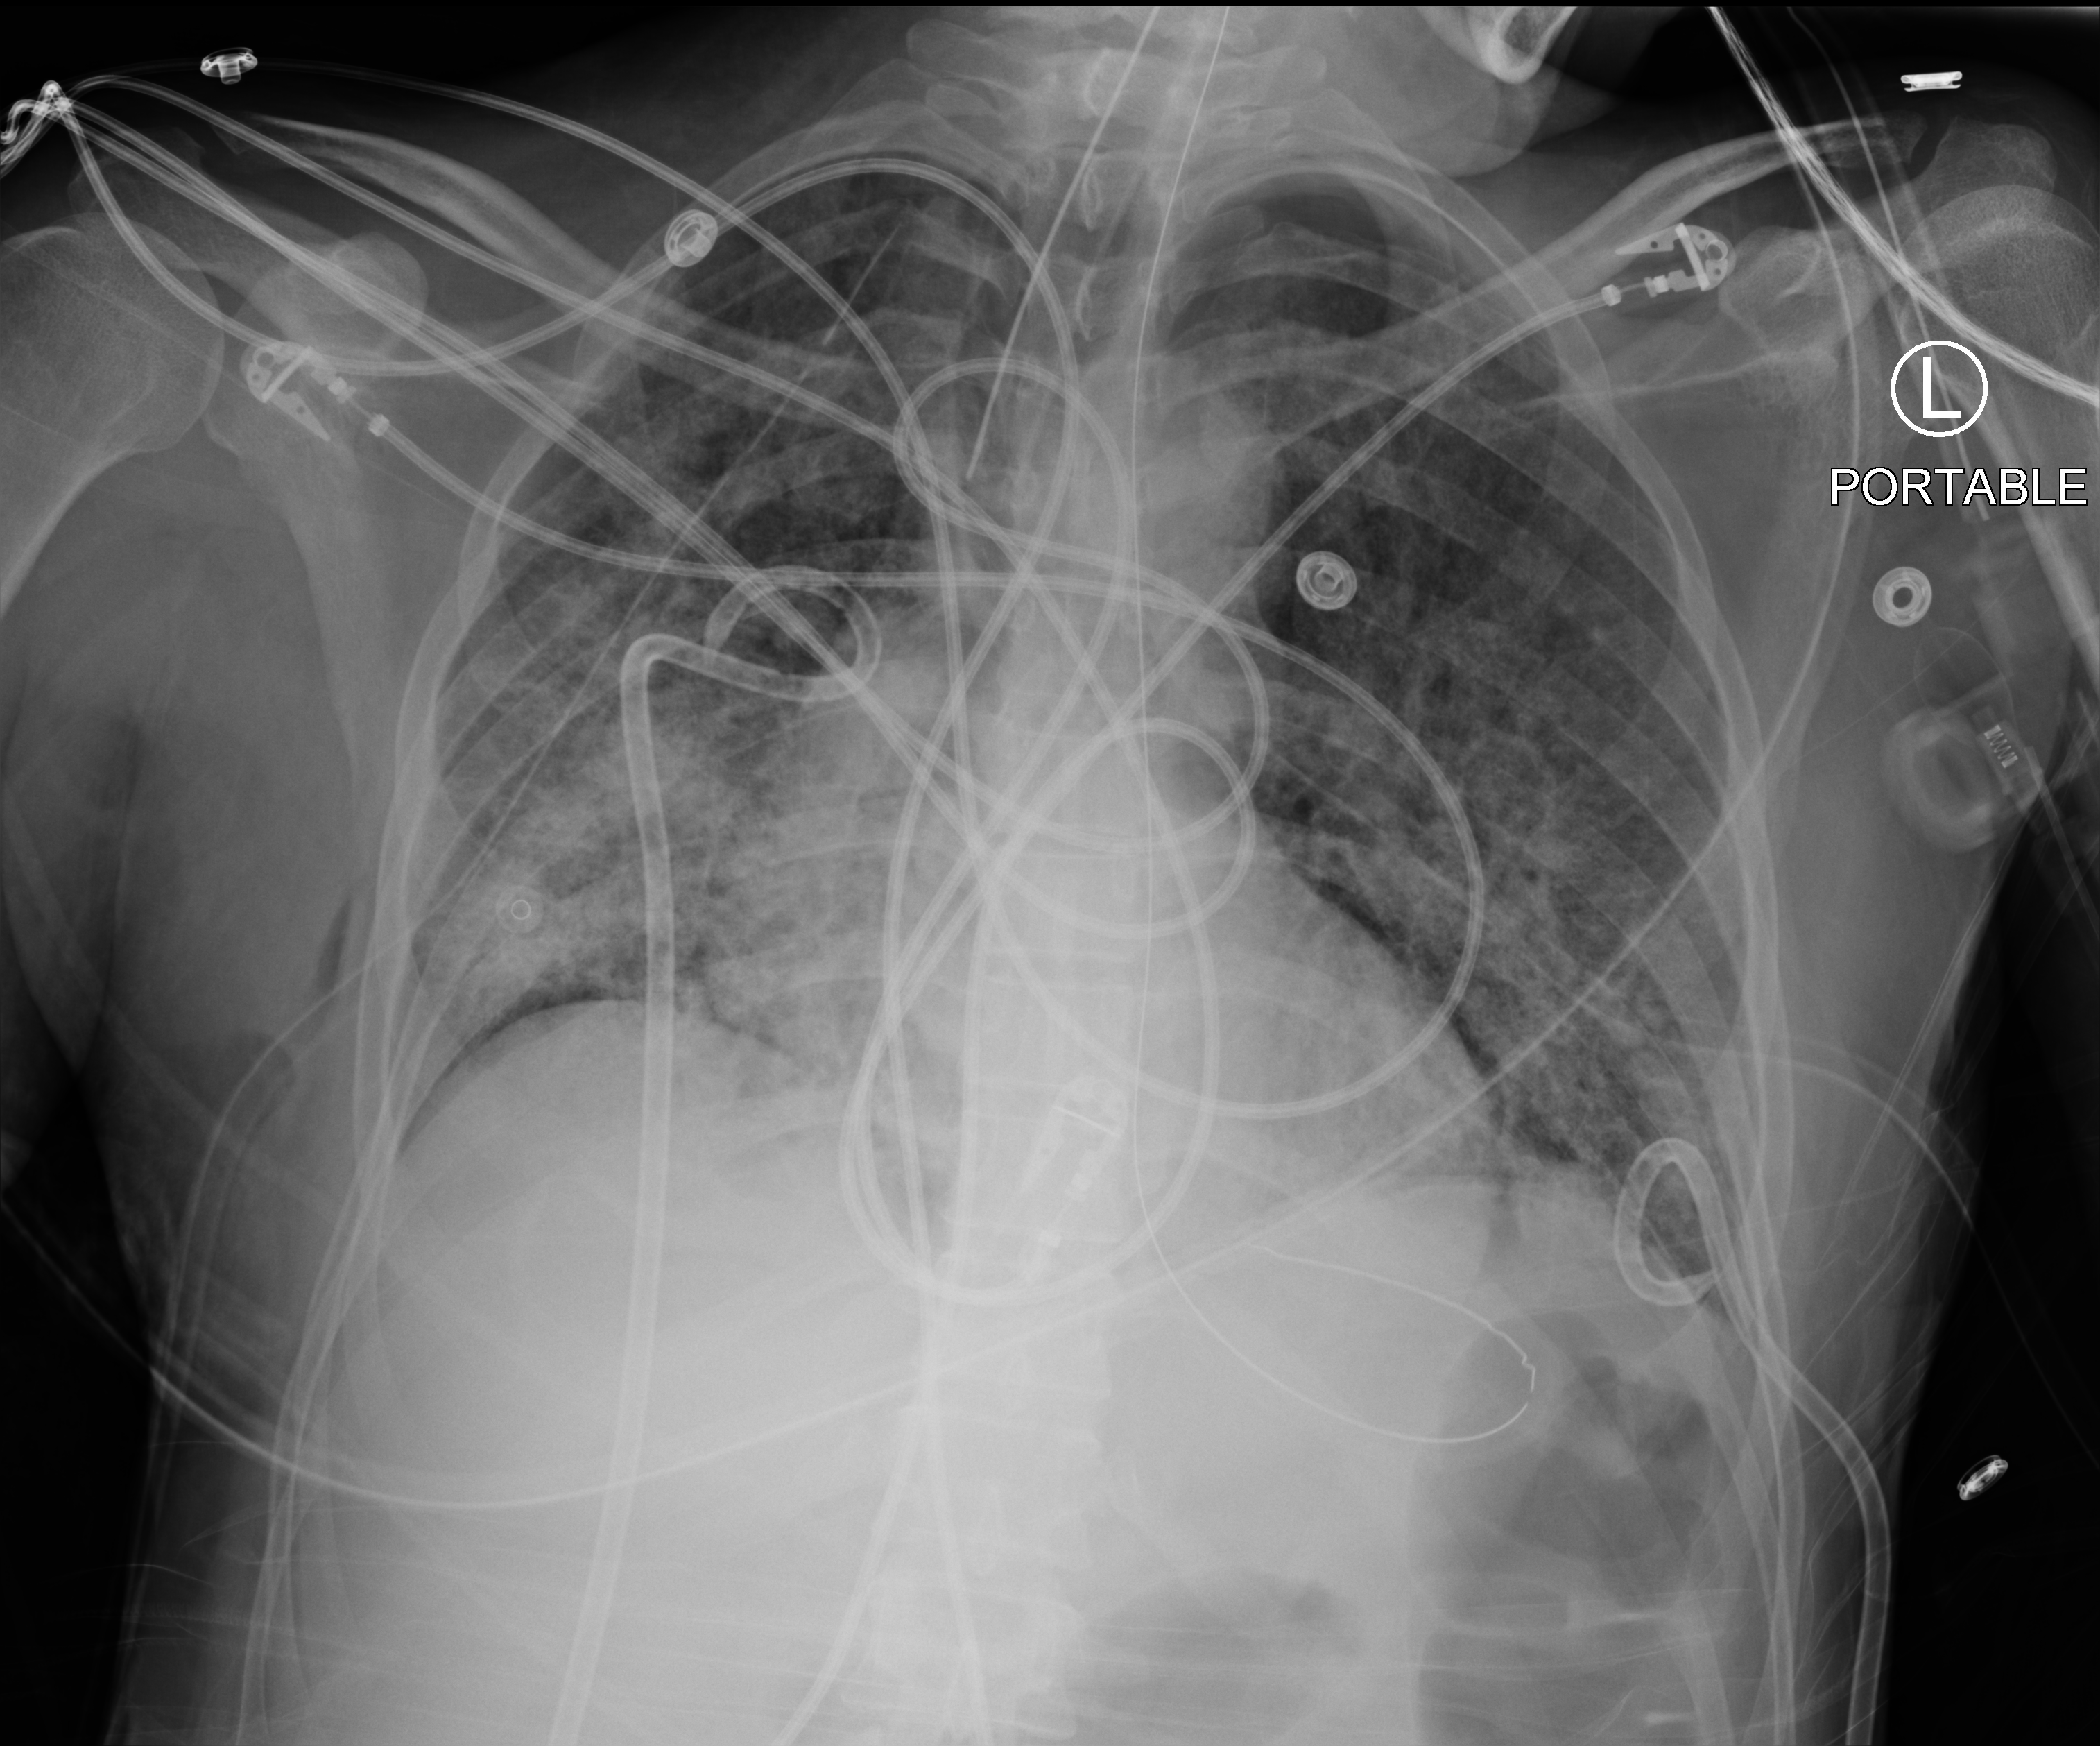
Chest X-ray (portable), anteroposterior (AP) projection. Patient hospitalised with COVID-19, aged 18–59 years.
From the hospital-stay record, not from the radiograph (when in the stay this image was taken is not recorded): admitted to intensive care during this hospital stay: yes; hypertension (admission record): no; mechanically ventilated during this hospital stay: yes.